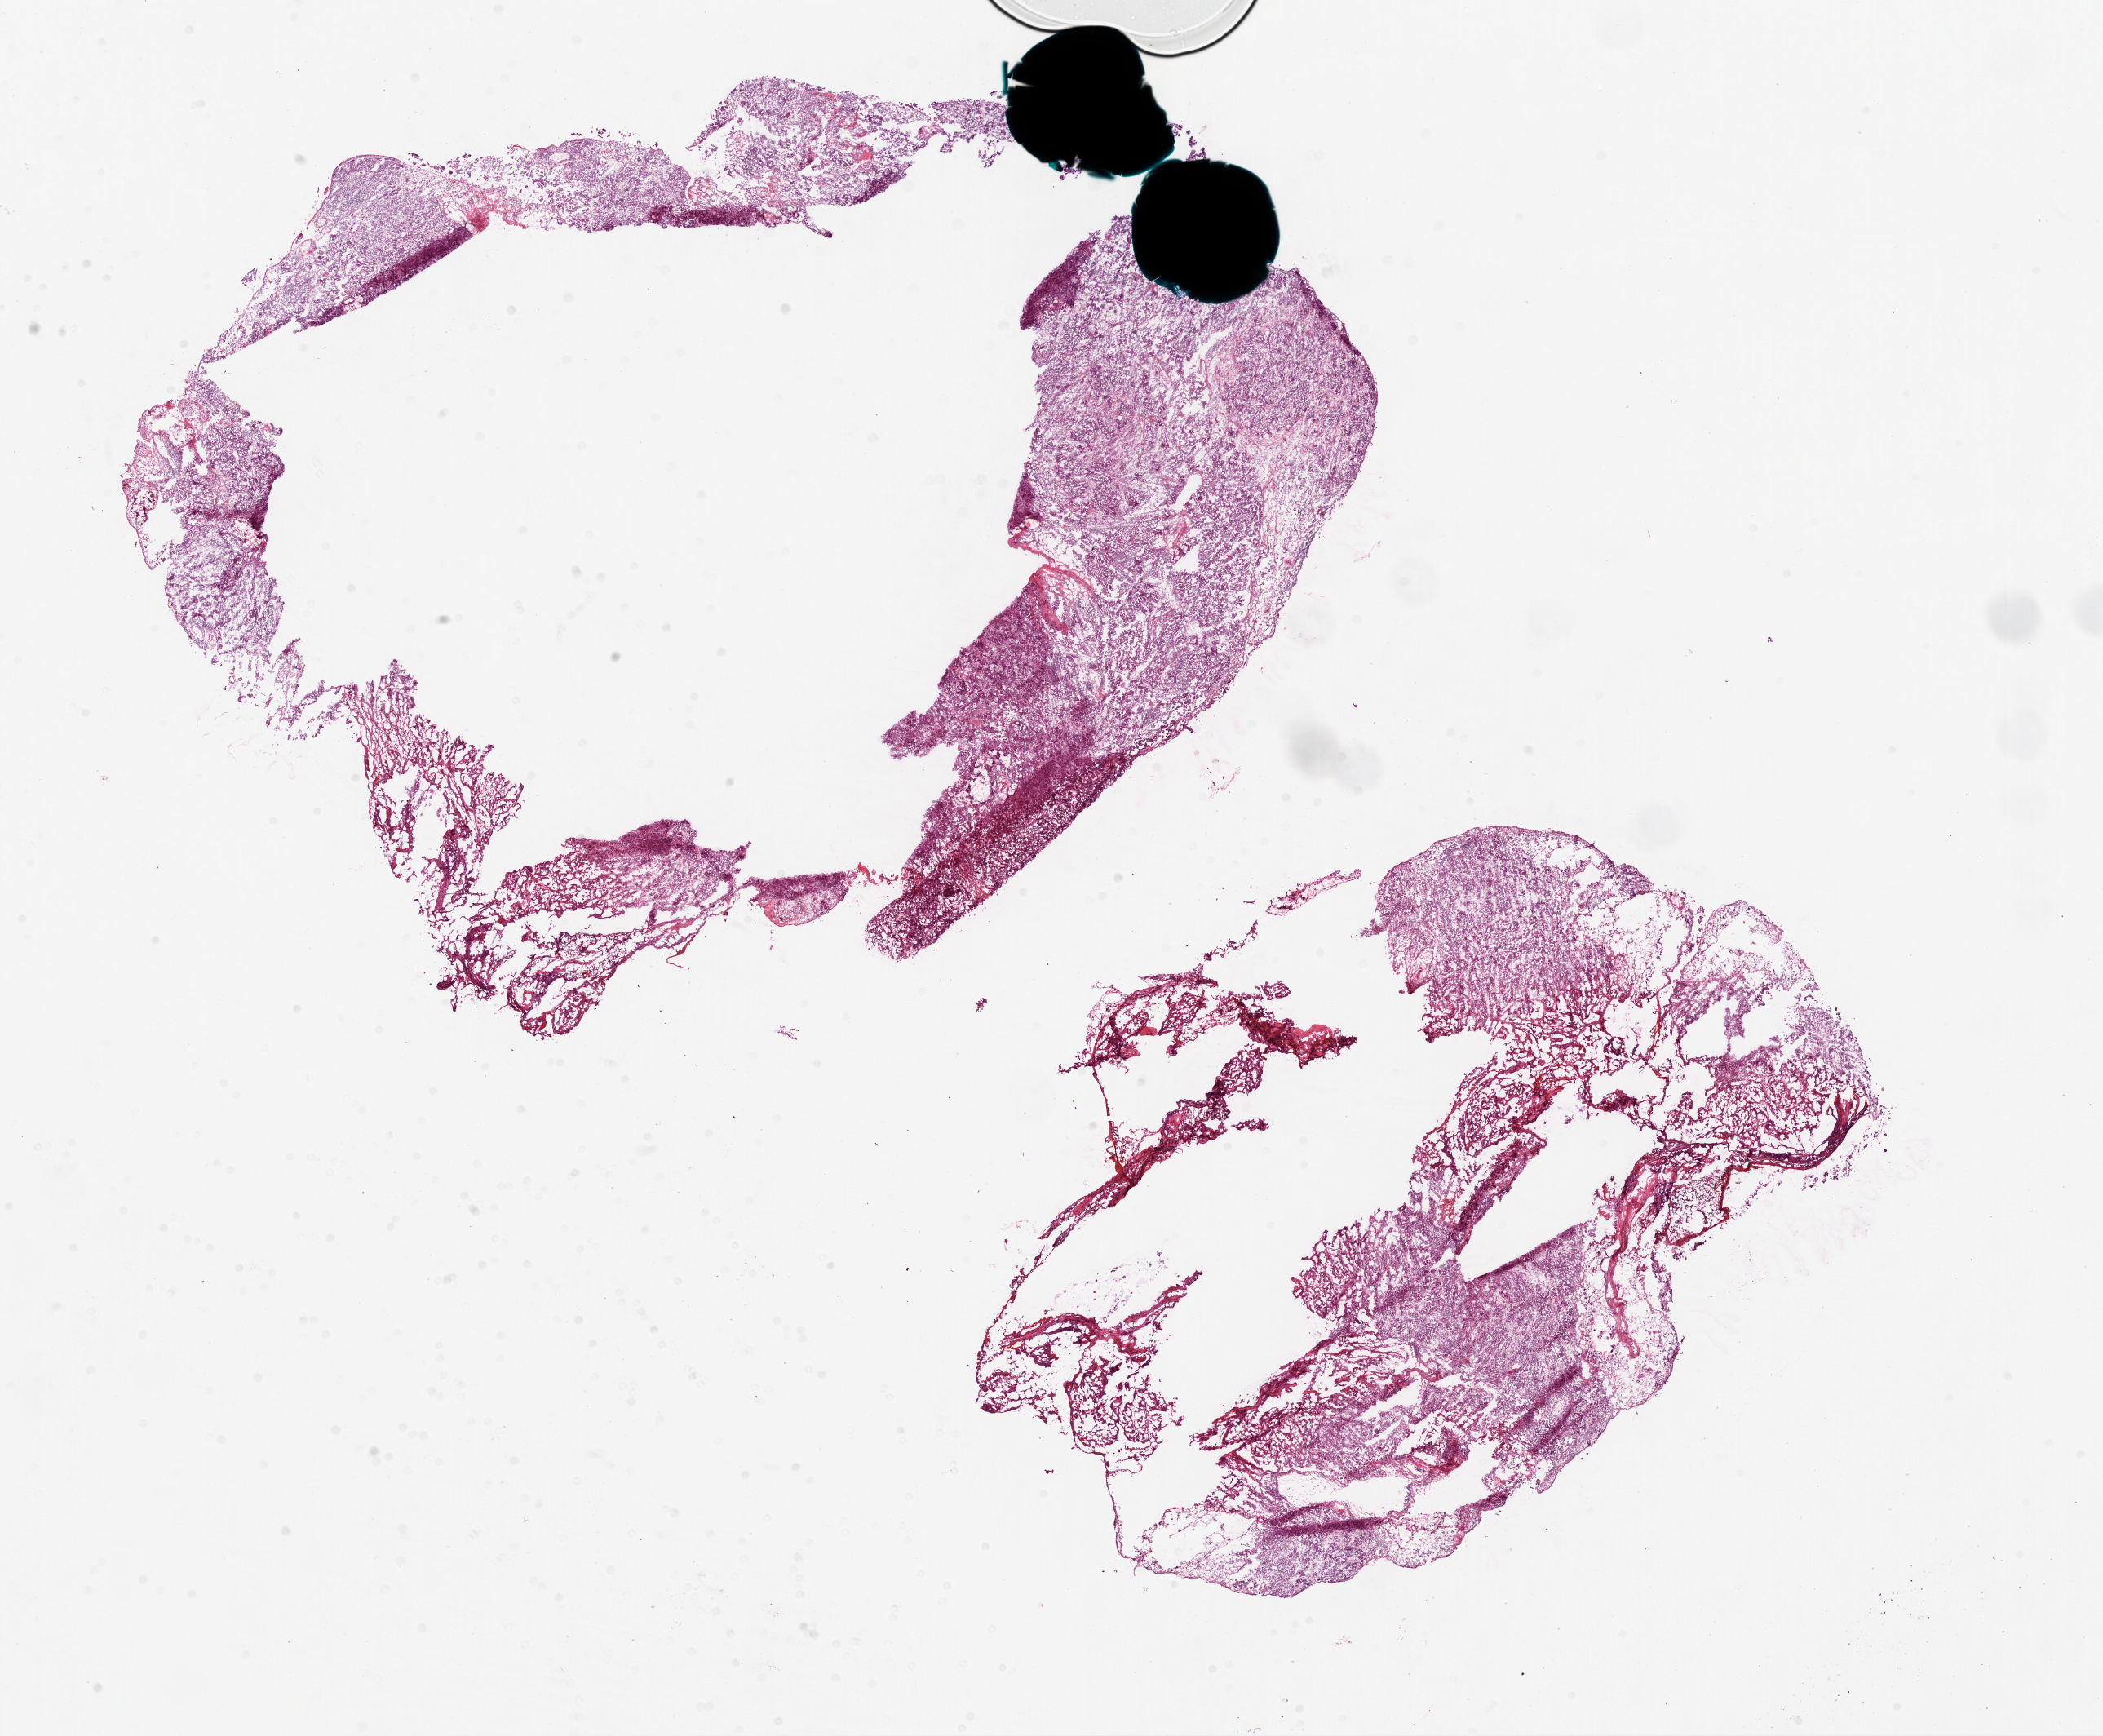
Hematoxylin and eosin (H&E) stained whole-slide image — whole scanned area (about 20.8 x 17.2 mm) shown as a low-resolution overview, frozen section from the bottom of the tissue portion, ovary, primary tumour sample. Female patient; age at initial diagnosis 45 years. Histologic grade: G3 (poorly differentiated). Pathologist review of this section (percent, as recorded): tumour cells 65%, tumour nuclei 70%, normal cells 0%, stromal cells 35%, necrosis 0%.
- histologic diagnosis: Serous cystadenocarcinoma, NOS
- FIGO stage: IV